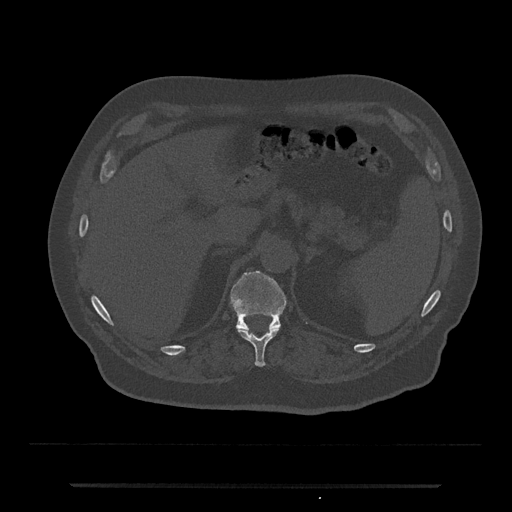
CT including the spine, one axial slice; slice 623 of 797 in the series (ordered by position); reconstruction kernel Br40s/3; 120 kVp; bone window (W 1800 / L 400 HU); 512 × 512 image matrix, field of view 434 × 434 mm. Patient: male, 80 years. From the clinical record (not read from this slice): primary cancer: prostate; vertebrae with lytic lesions (as recorded): L1, T11.
Structures marked on this image (semi-automatic segmentation, software-assisted and operator-edited):
- T11 vertebra: bounding box [x1, y1, x2, y2] px = [237, 328, 280, 367]
- T12 vertebra: [230, 270, 287, 331]